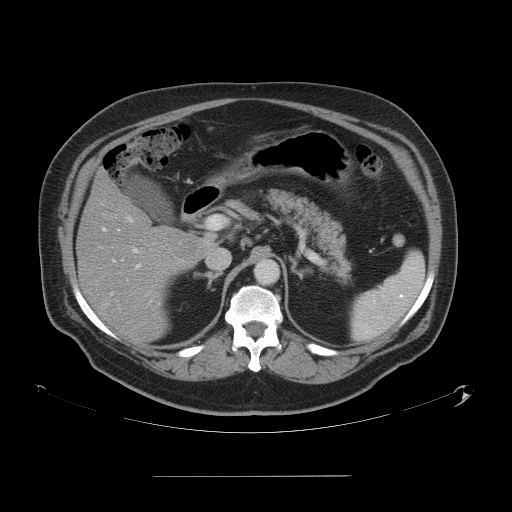
Contrast-enhanced abdominal CT, one axial slice; 120 kVp; intravenous contrast given; soft-tissue window (W 400 / L 40 HU); 5 mm slice thickness; 512 × 512 image matrix. Male patient, age 63 years. From the clinical record (not read from this slice): diagnosis: colorectal cancer liver metastases, imaged before liver resection.
Outlined on this slice (manually delineated by an expert):
- hepatic veins: bounding box <110,292,117,301> (left, top, right, bottom; pixels)
- liver: <78,173,208,340>
- planned liver remnant (the part of the liver to remain after resection): <78,184,203,340>
- portal vein (with intrahepatic branches): <102,228,151,292>